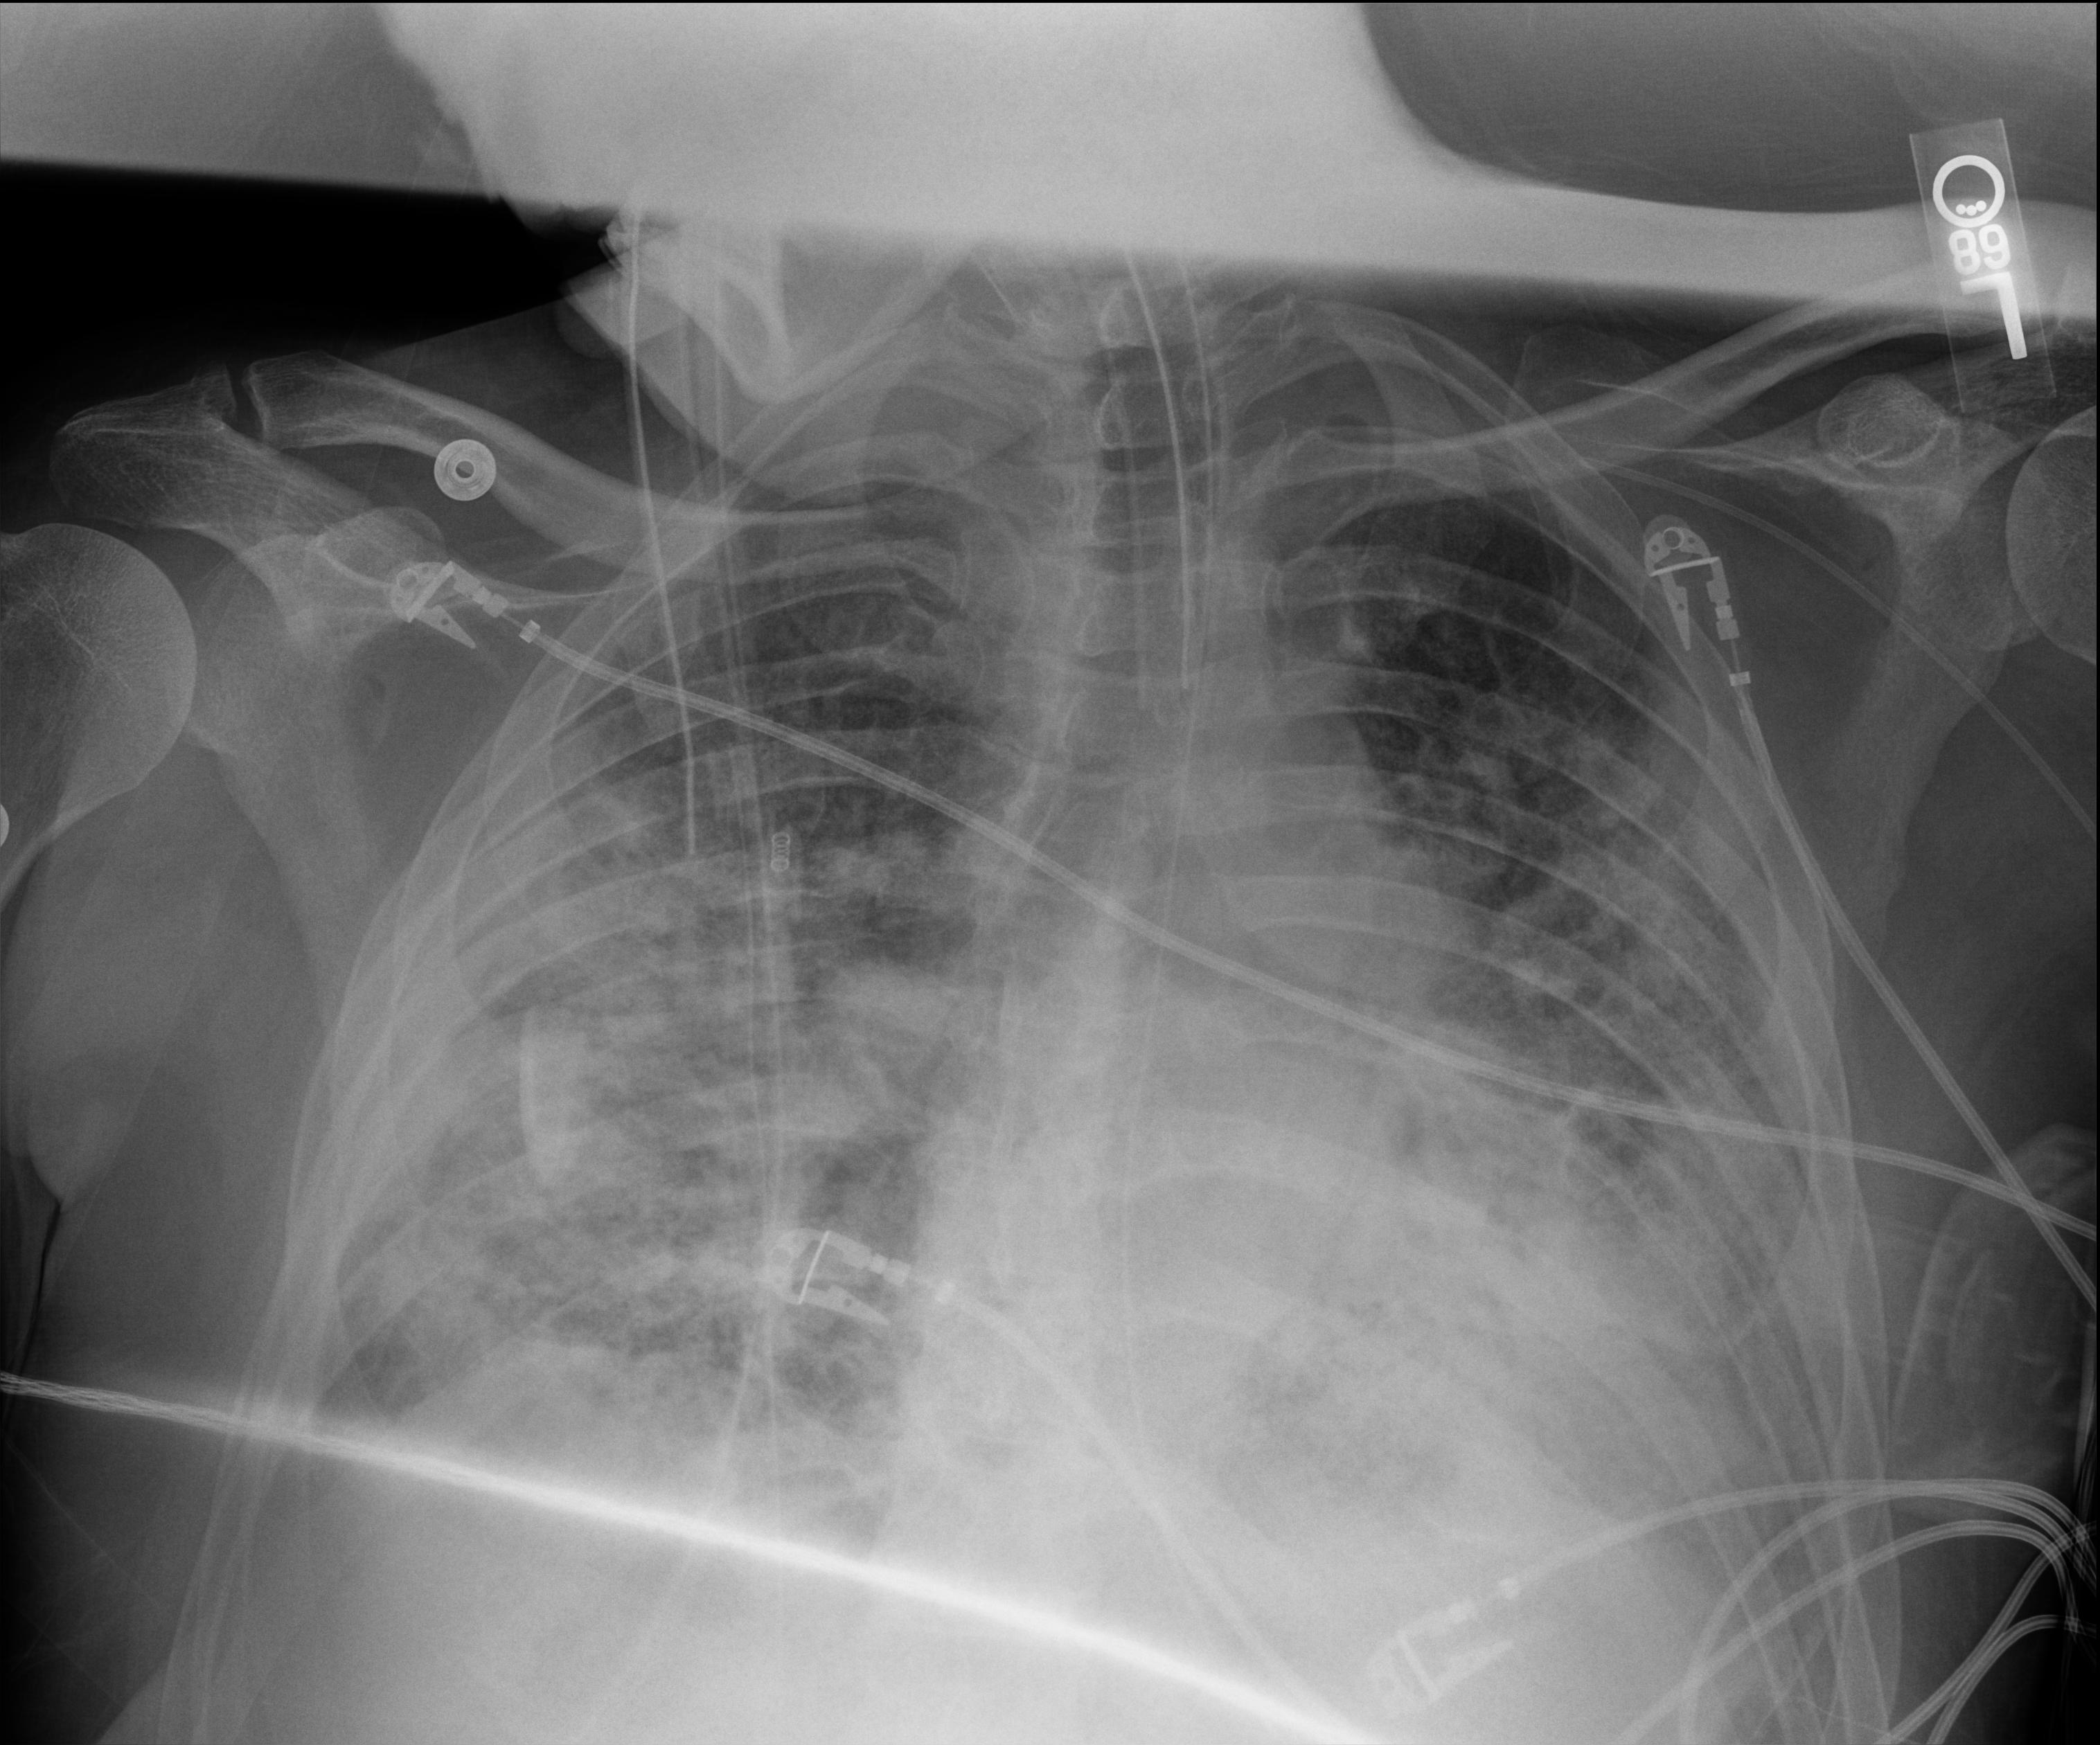
Portable chest radiograph; anteroposterior (AP) projection. Male patient hospitalised with COVID-19, age 18–59 years.
From the hospital-stay record, not from the radiograph (when in the stay this image was taken is not recorded):
- length of hospital stay: 75 days
- mechanically ventilated during this hospital stay: yes